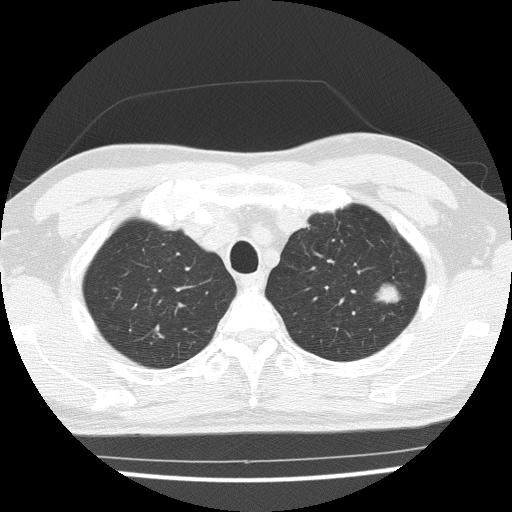
Low-dose screening chest CT, axial slice; third screening round (two years after baseline); lung window (W 1500 / L -600 HU); 2 mm slice thickness; lung (sharp) reconstruction kernel (FC51). Male, age 65 years at enrolment. Current smoker at enrolment.
Expert-annotated lung lesion, bounding box <359,273,413,320> (left, top, right, bottom; pixels). Screening reader's record for this exam (one nodule recorded; not confirmed to be the boxed lesion): non-calcified nodule or mass ≥4 mm, left upper lobe, 16 × 15 mm, poorly defined margins, soft tissue attenuation, pre-existing on the prior screen: yes; interval growth: yes. Official screen result: positive, other.